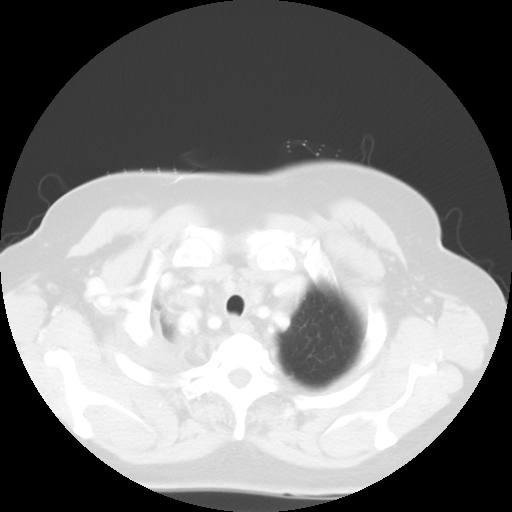
Chest CT, one axial slice. Slice 48 of 52 in the series (ordered by position). 120 kVp. Lung window (W 1500 / L -600 HU). 5 mm slice thickness. 512 × 512 image matrix. Patient: female, 81 years. From the clinical record (not read from this slice): clinical TNM (as recorded): T4 N3 M1b.
Outlined on this slice (bounding box drawn by a radiologist):
- lung tumour (recorded histology: adenocarcinoma): bounding box <150,308,209,377> (left, top, right, bottom; pixels)